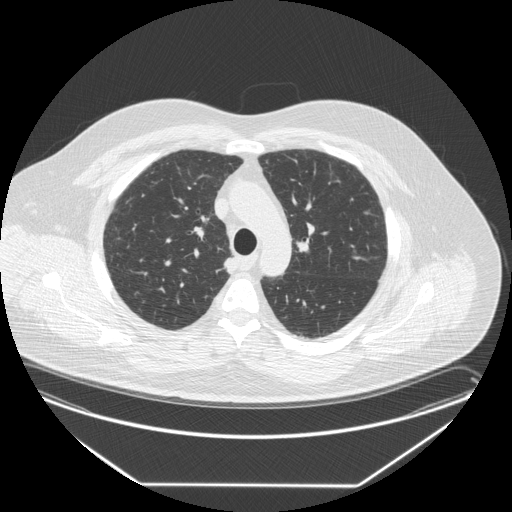
Low-dose screening chest CT, one axial slice. Position 197 of 258 along the scan axis. Lung window (W 1500 / L -600 HU). 2.5 mm slice thickness. 512 × 512 image matrix, field of view 440 × 440 mm.
Structures marked on this image (expert manual segmentation):
- lesion 1 (tumor, upper lobe of right lung): bounding box [x1, y1, x2, y2] px = [224, 254, 237, 274]